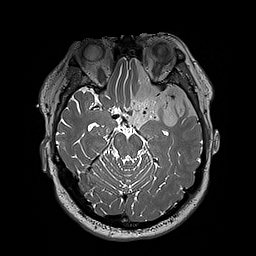
Brain MRI from a brain-tumour surgery series, one axial slice. Slice 133 of 192 in the series (ordered by position). 1 mm slice thickness. 256 × 256 image matrix, field of view 250 × 250 mm. Case-level facts recorded for this patient, not image findings: histopathology: Oligodendroglioma; WHO grade: 3; IDH mutation: yes.
Annotated regions visible in this slice (outlined manually by an expert reader):
- tumour: bounding box (x1, y1, x2, y2) in pixels: (124, 59, 197, 129)